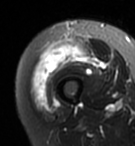
MRI of an extremity soft-tissue mass, one axial slice. Slice 20 of 95 in the series (ordered by position). T2-weighted fat-saturated. MR volume resampled by the dataset authors to the PET/CT grid (not the native acquisition matrix). 3.27 mm slice thickness. 135 × 146 image matrix, field of view 132 × 143 mm. Female patient. From the clinical record (not read from this slice): histological type: pleiomorphic undifferentiated sarcoma; grade: high; site of the primary tumour: right quadricep.
Structures marked on this image (expert contour drawn on MRI and transferred to this co-registered scan by the dataset authors):
- gross tumour volume including surrounding oedema: bounding box <32,38,88,108> (left, top, right, bottom; pixels)